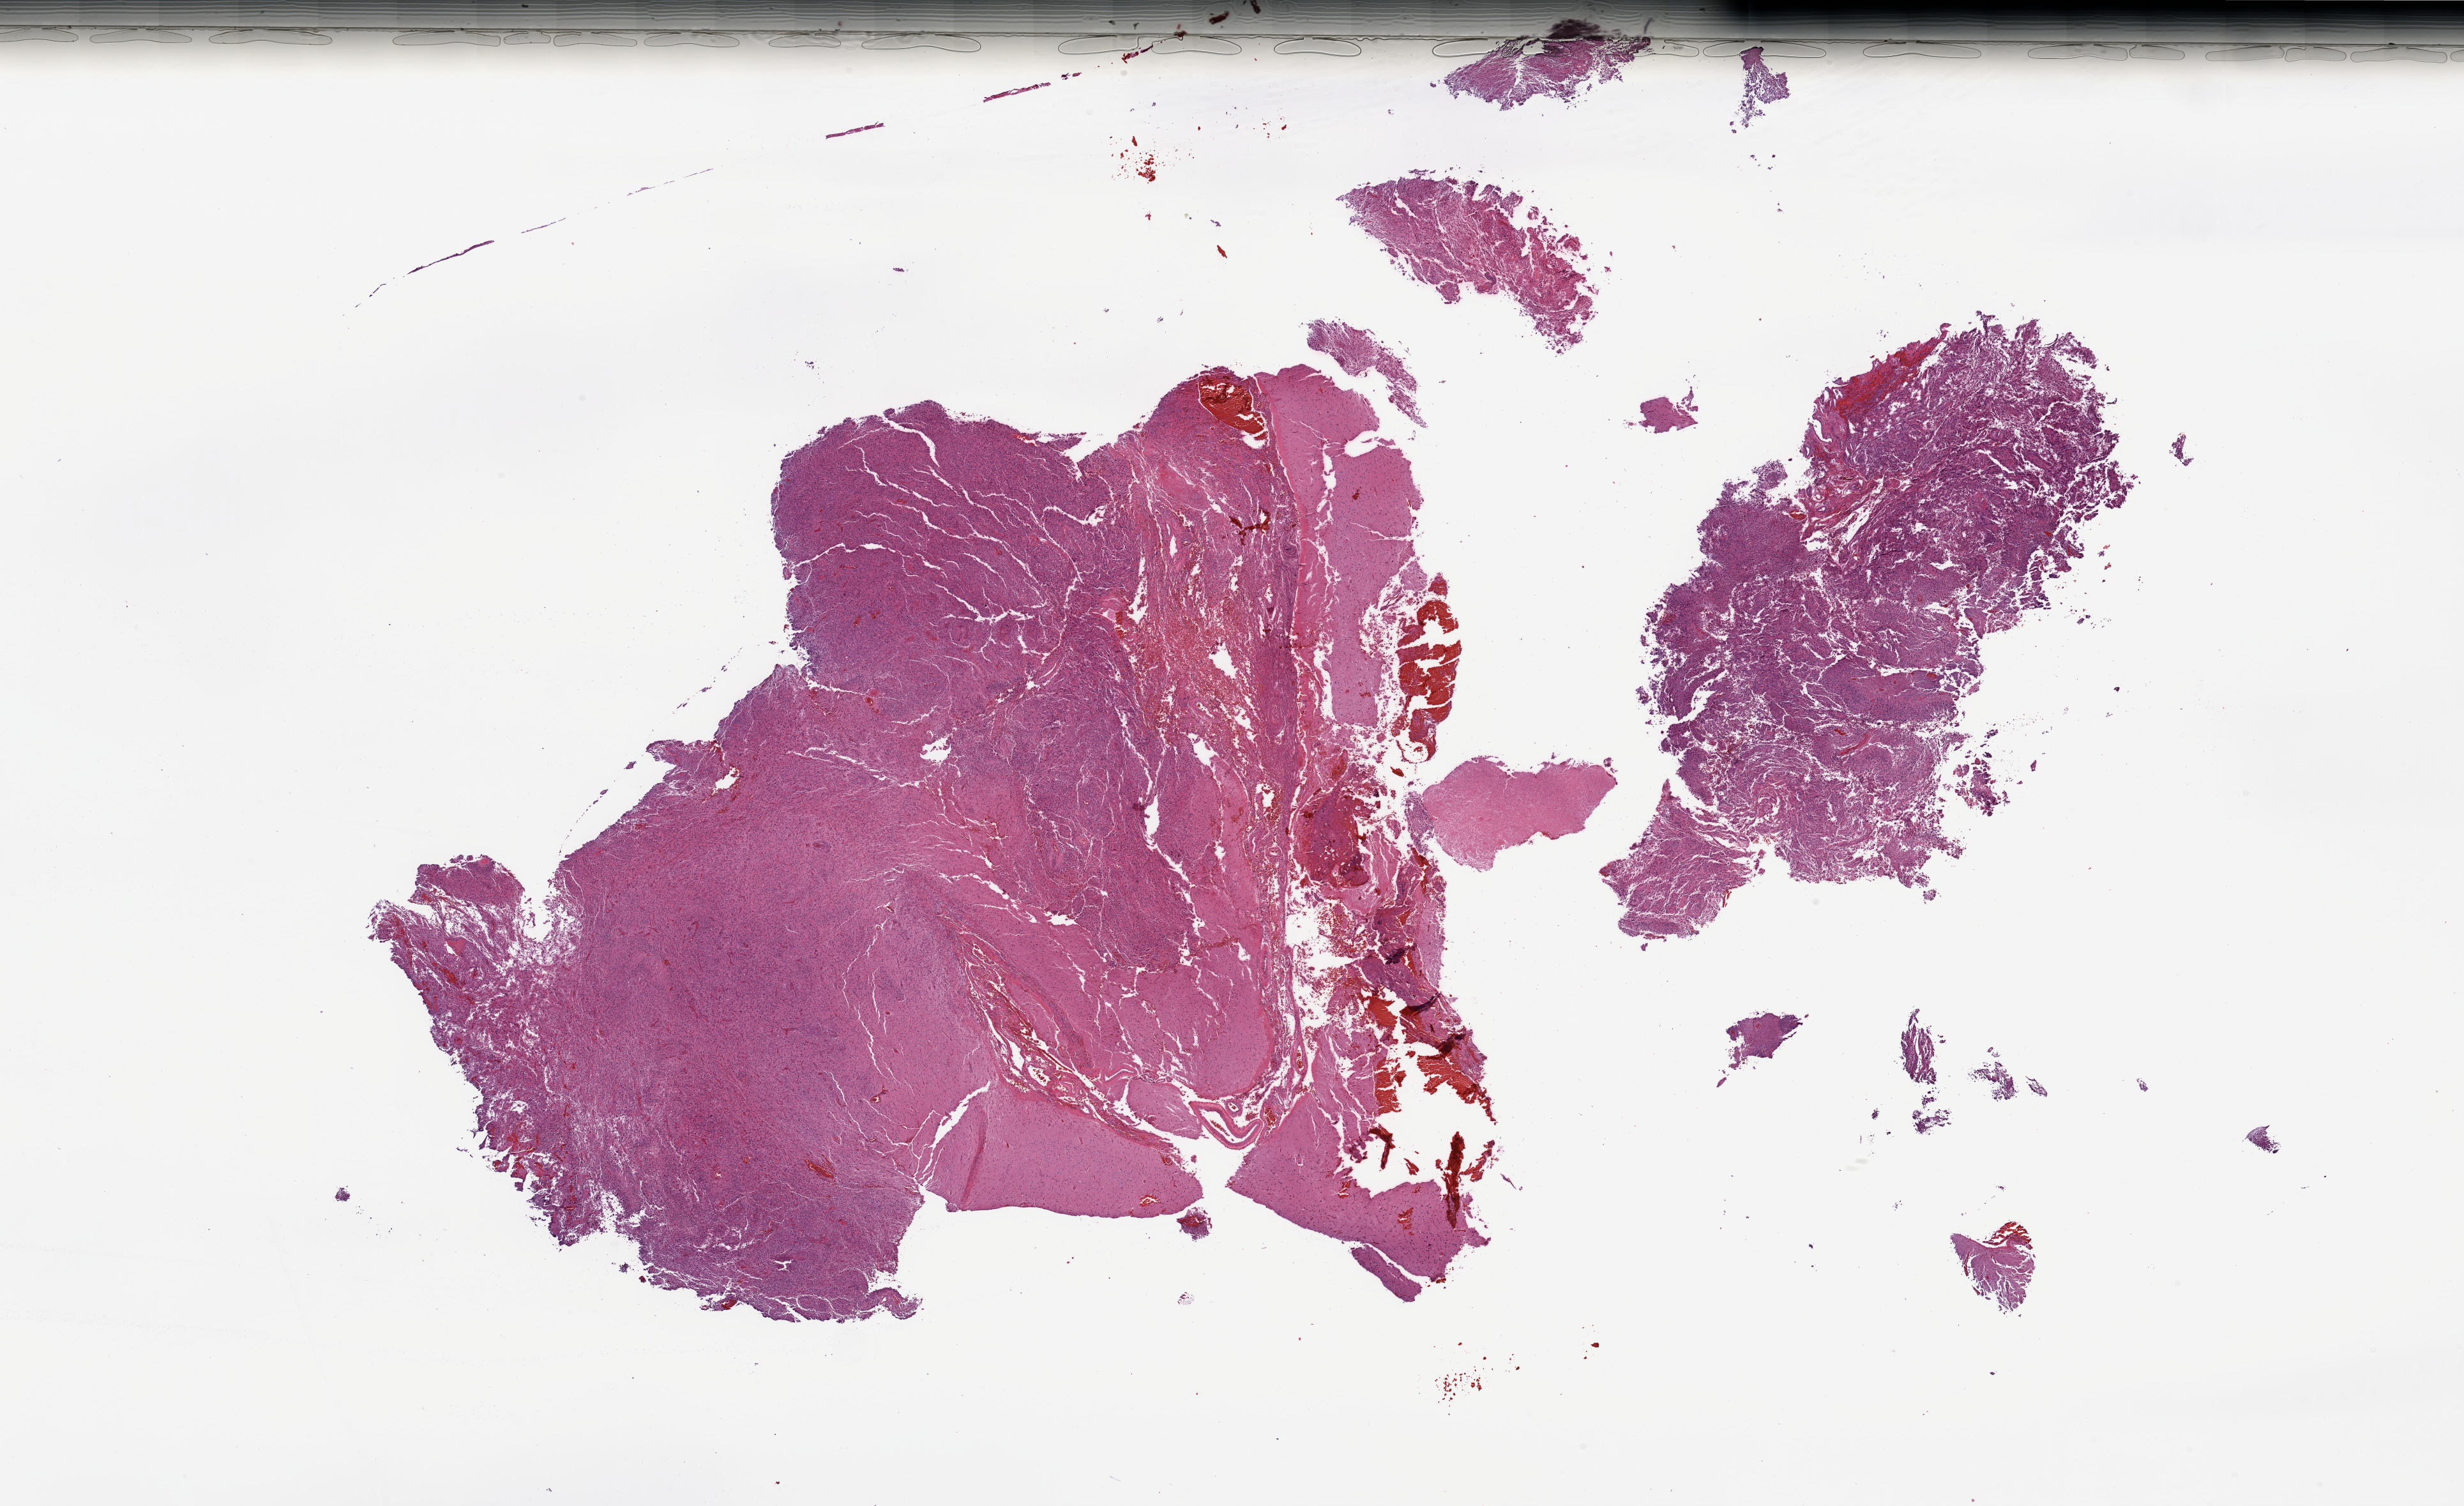
Whole-slide histology image, H&E-stained, low-resolution overview of the scanned area, about 30.5 x 18.6 mm (acquisition: 20x scan). Tumour tissue sample, sampled site: brain. Male, 75 y/o. Pathologist review of this section (percent, as recorded): tumour nuclei 75%, necrosis 20%.
Diagnosis: Glioblastoma. Primary tumour site (as recorded): temporal lobe.